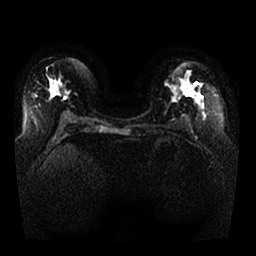
Breast MRI, one axial slice. Slice 16 of 25 in the series (ordered by position). Diffusion-weighted series; image 2 of 4 stored at this slice position (different b-values; order by instance number). 1.5 T. 4 mm slice thickness. 256 × 256 image matrix, field of view 350 × 350 mm. Female patient.
Outlined on this slice (outlined manually by an expert reader):
- tumour on diffusion-weighted imaging: box from (x=183, y=85) to (x=194, y=95) px